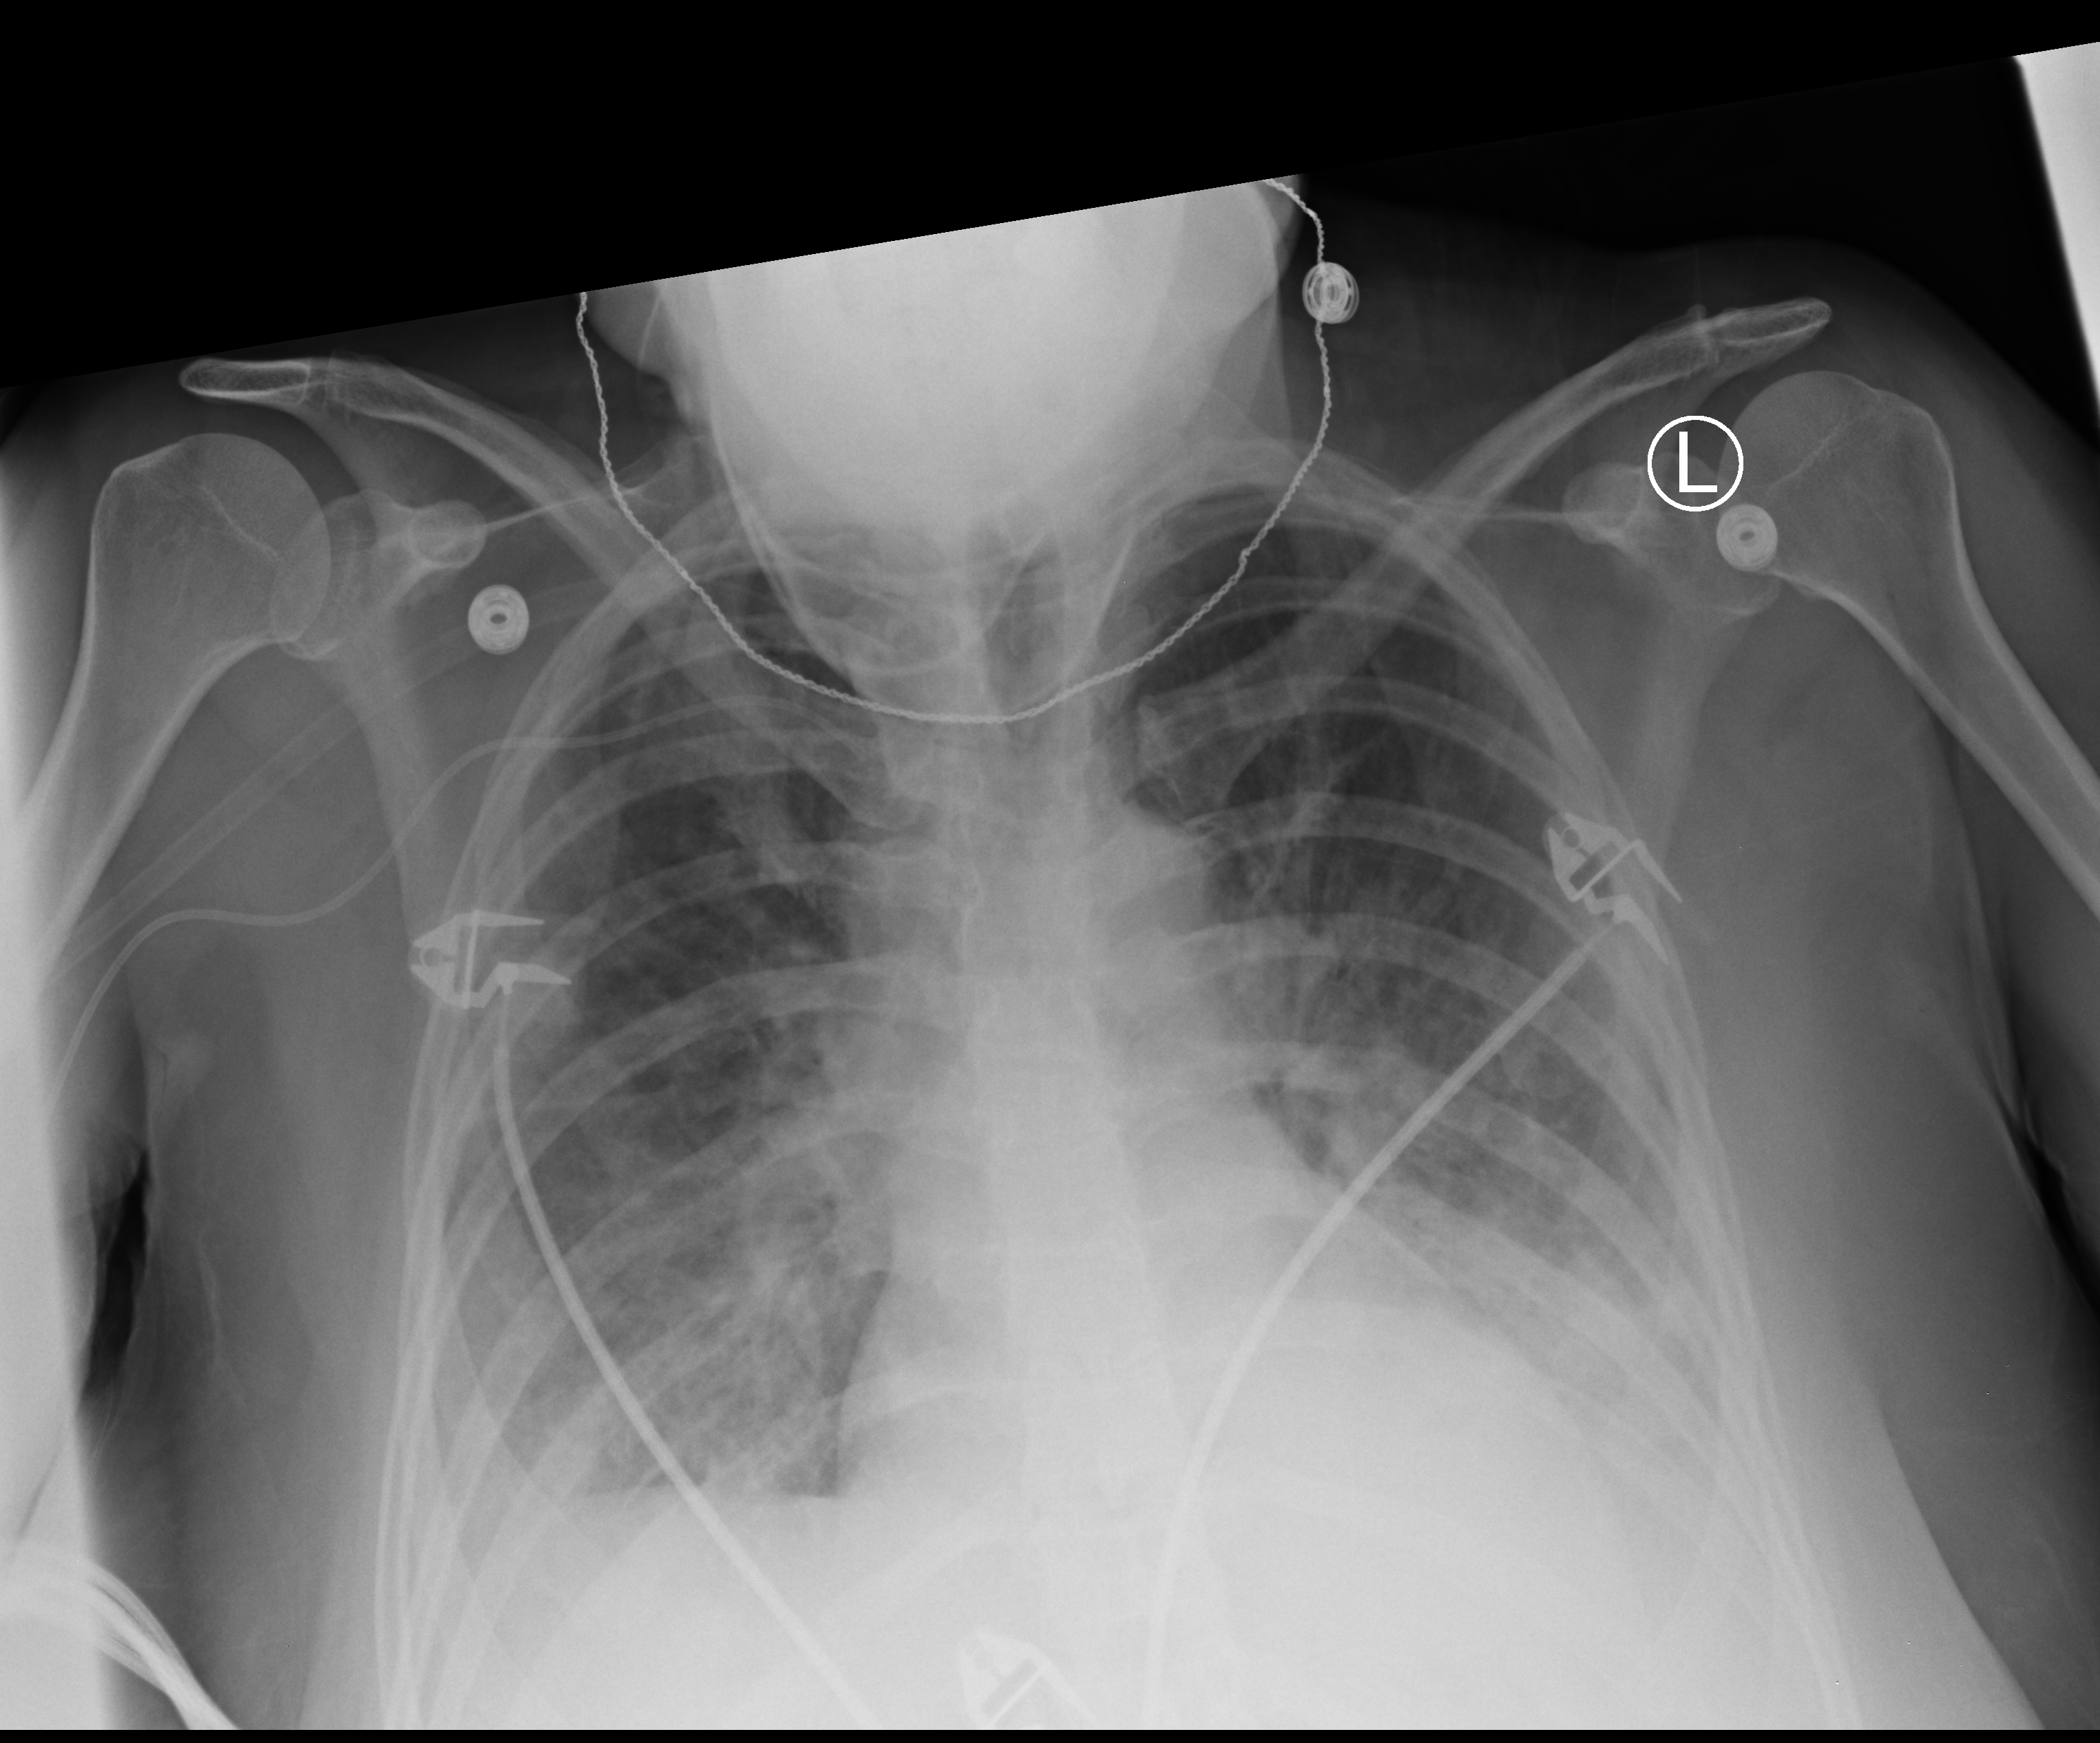
Bedside chest radiograph (computed radiography); anteroposterior (AP) projection. Patient hospitalised with COVID-19; female, aged 18–59 years.
From the hospital-stay record, not from the radiograph (when in the stay this image was taken is not recorded):
- smoking status (admission record): never
- other chronic lung disease (admission record): no